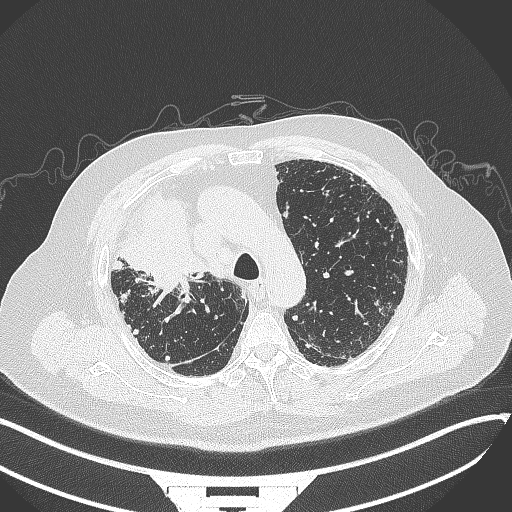
Chest CT, one axial slice. Slice 259 of 384 in the series (ordered by position). Reconstruction kernel B70f. 120 kVp. Lung window (W 1500 / L -600 HU). 1 mm slice thickness. 512 × 512 image matrix, field of view 400 × 400 mm. Male patient, age 69 years. From the clinical record (not read from this slice): clinical TNM (as recorded): T4 N3 M1.
Annotated regions visible in this slice (bounding box drawn by a radiologist):
- lung tumour (recorded histology: adenocarcinoma): box from (x=118, y=193) to (x=208, y=303) px